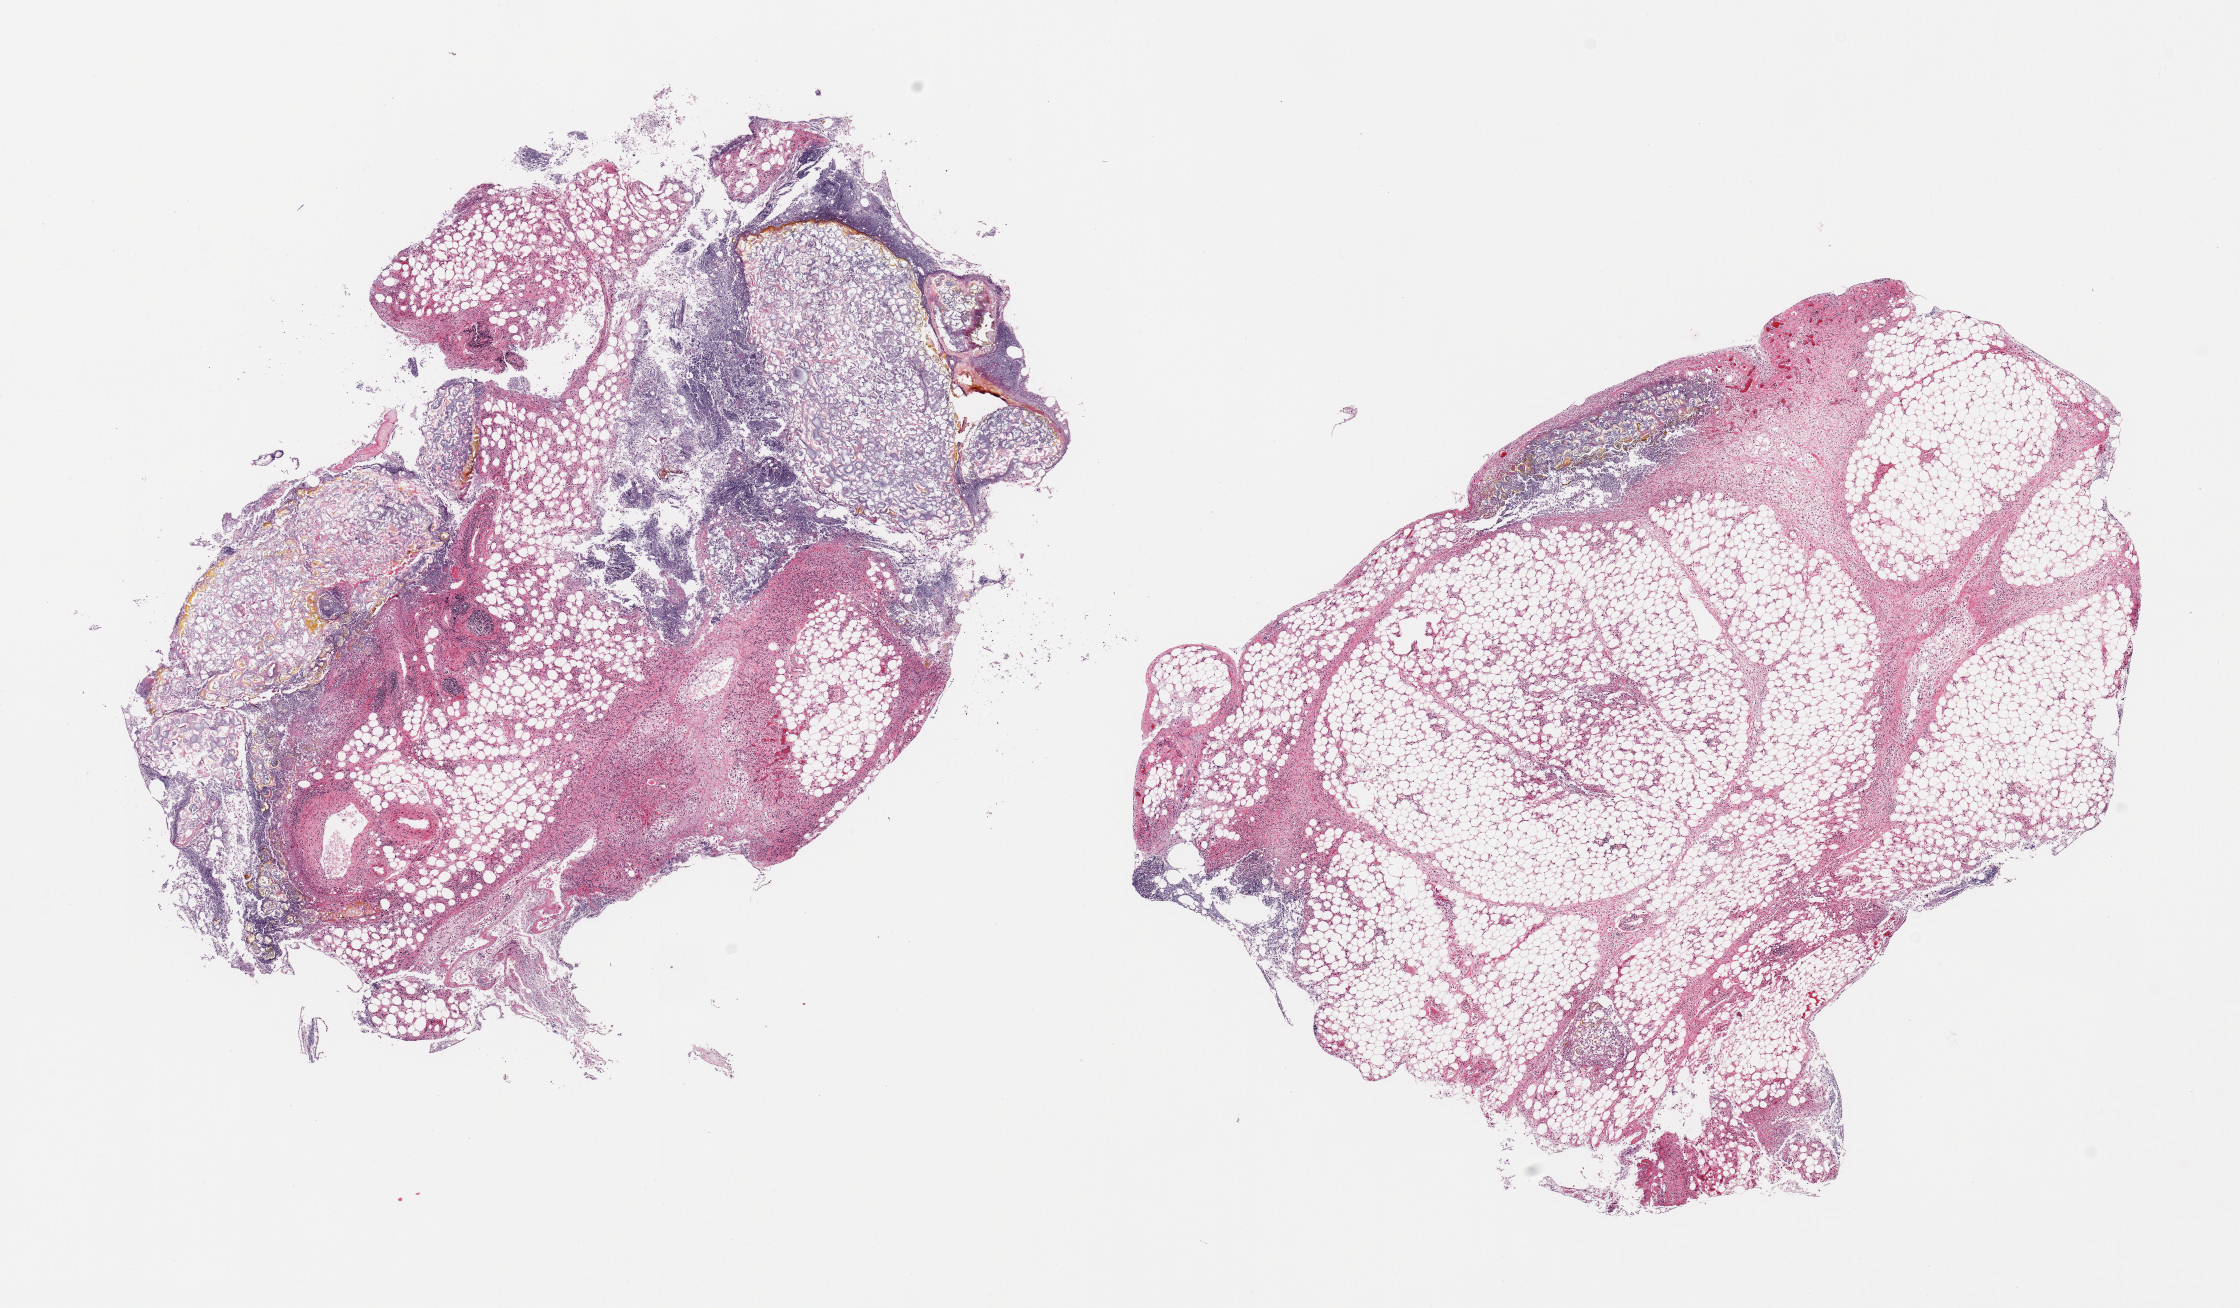
Digitized haematoxylin and eosin-stained section, brightfield — a low-resolution overview of the entire scanned area, about 17.7 x 10.3 mm (from a 20x scan). PAXgene-fixed paraffin-embedded (PFPE) section. Sampled site (target tissue): pancreas. Donor tissue sample. Donor: male.
Pathologist's review note for this sample: 2 pieces, ~20% completely saponified pancreas, mainly fibroadipose tissue with fat necrosis.